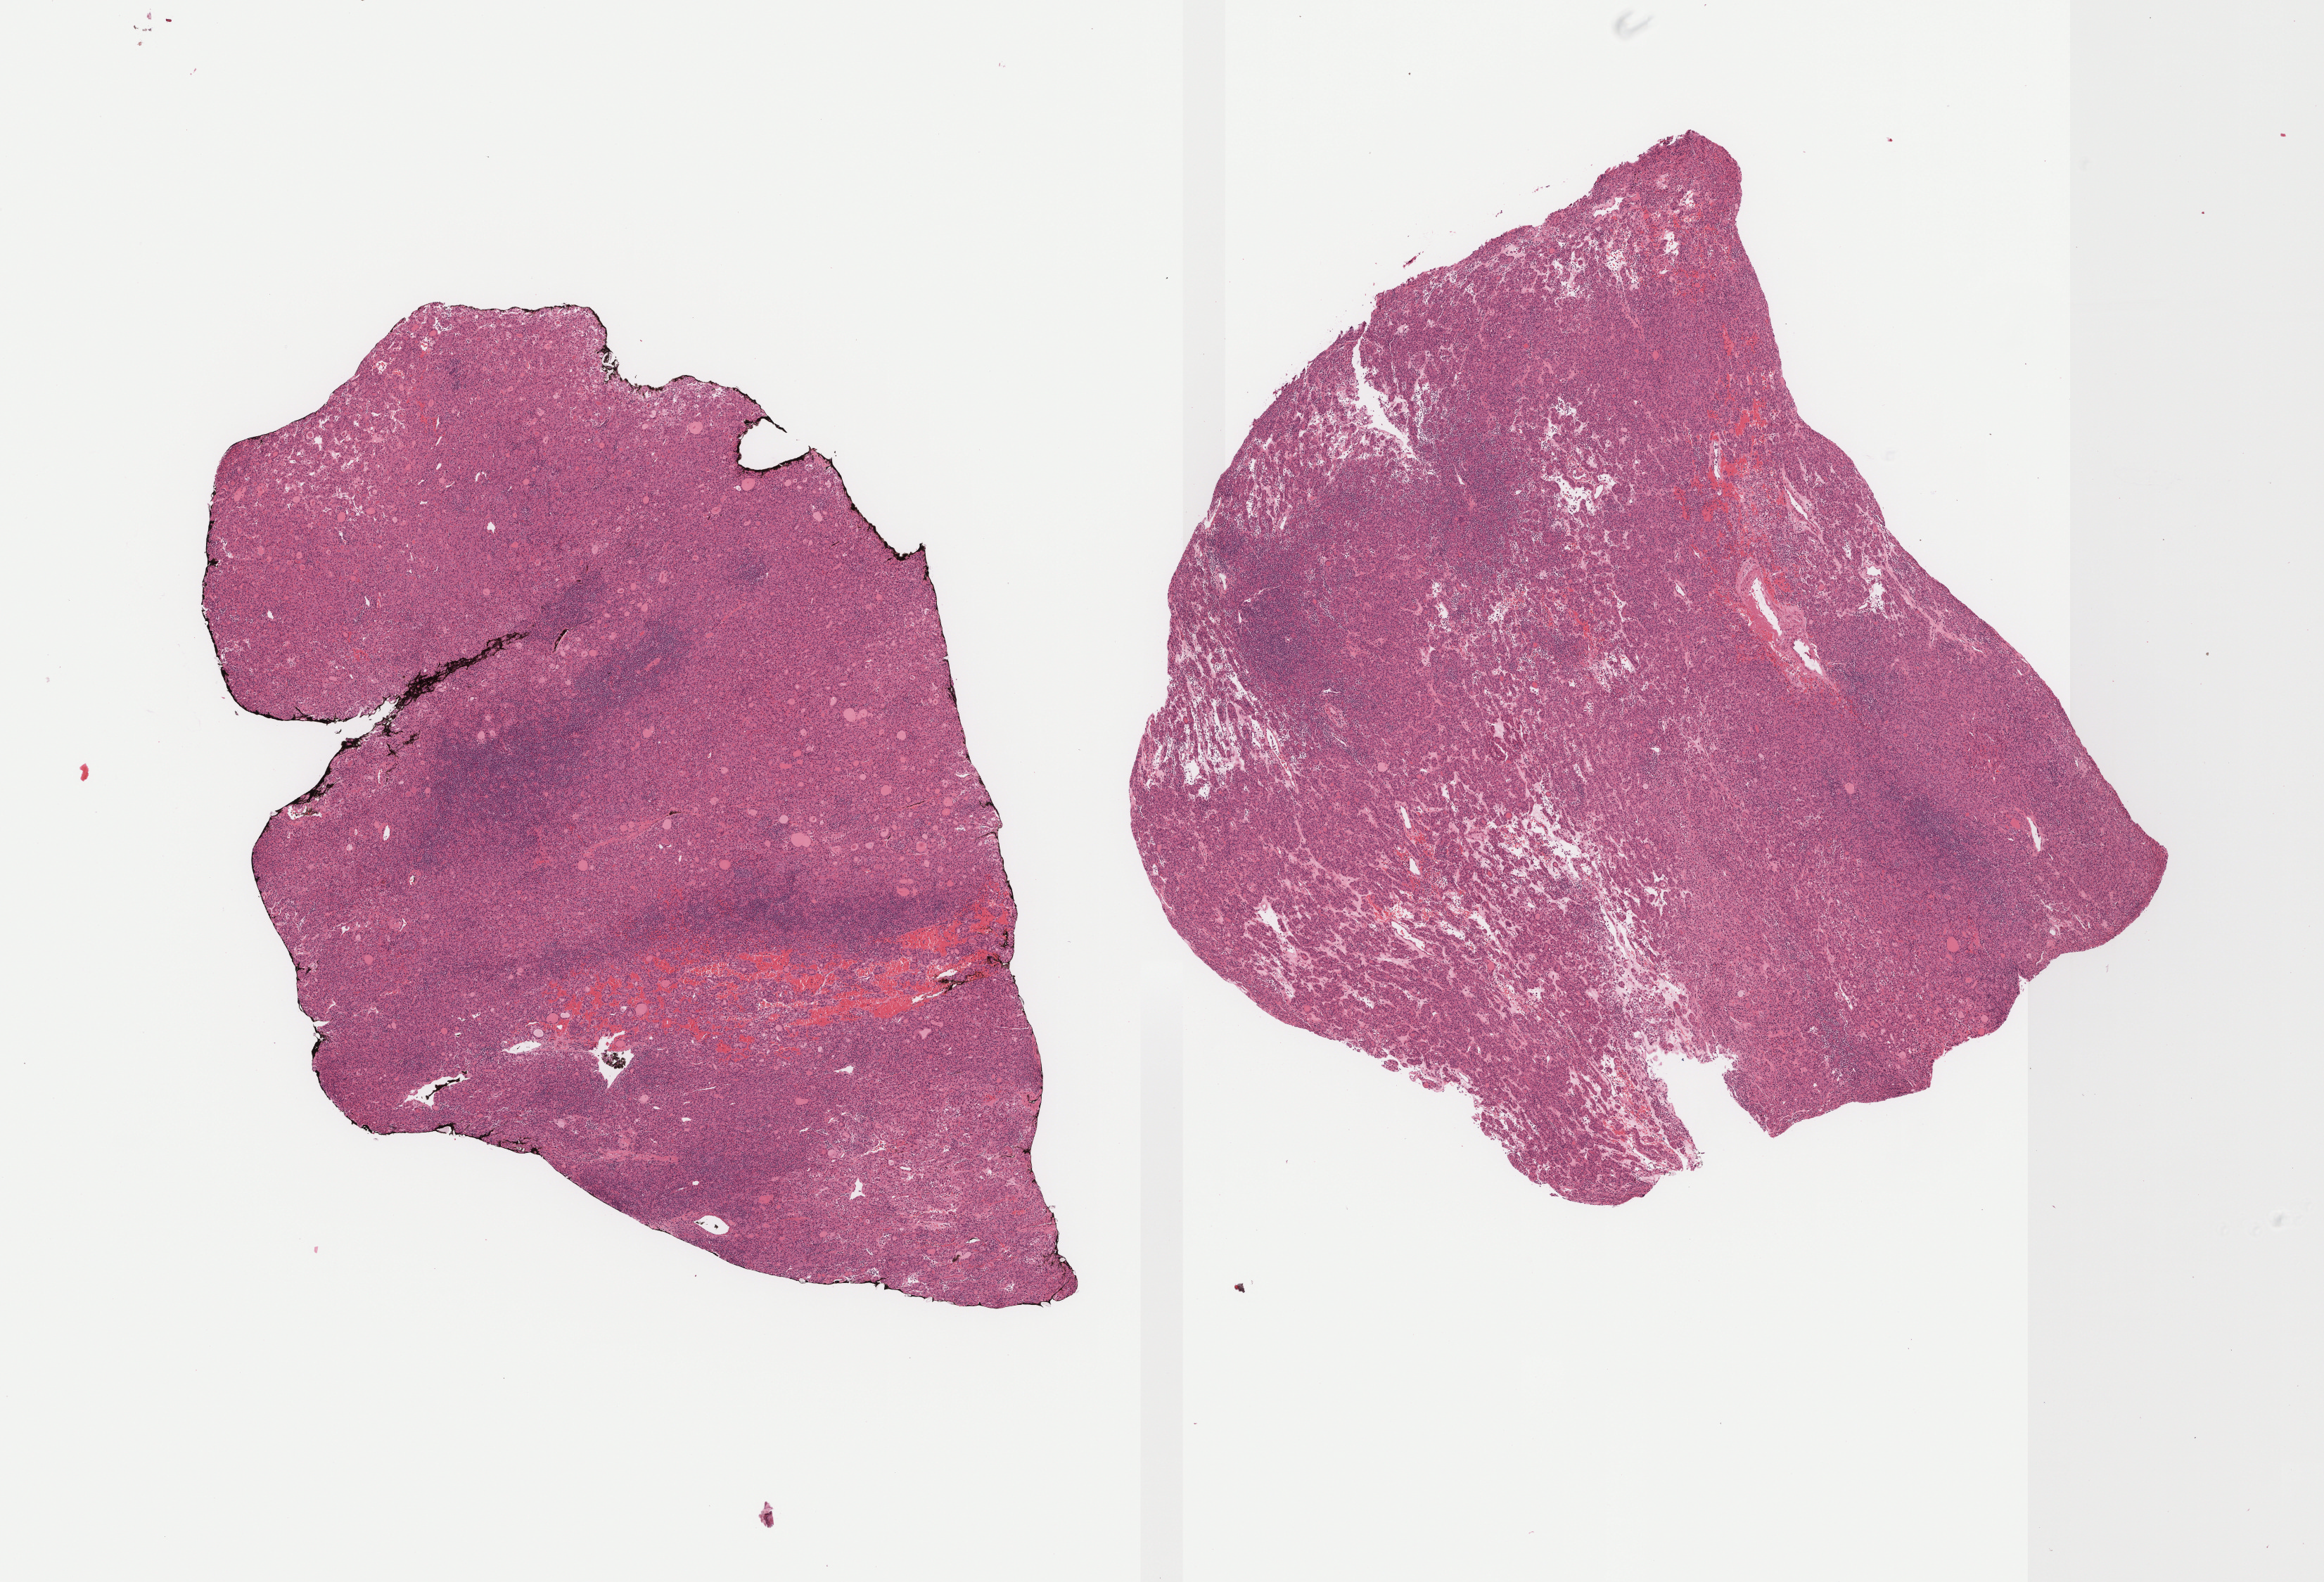
H&E whole-slide image, low-resolution overview of the scanned area, about 13.3 x 9.1 mm, formalin-fixed paraffin-embedded (FFPE) diagnostic section, primary tumour sample from the thyroid. Female patient; age at initial diagnosis 26 years.
• laterality: left
• diagnosis: Papillary carcinoma, follicular variant (thyroid gland)
• TNM: T2 N0 MX
• AJCC pathologic stage: I (7th edition)